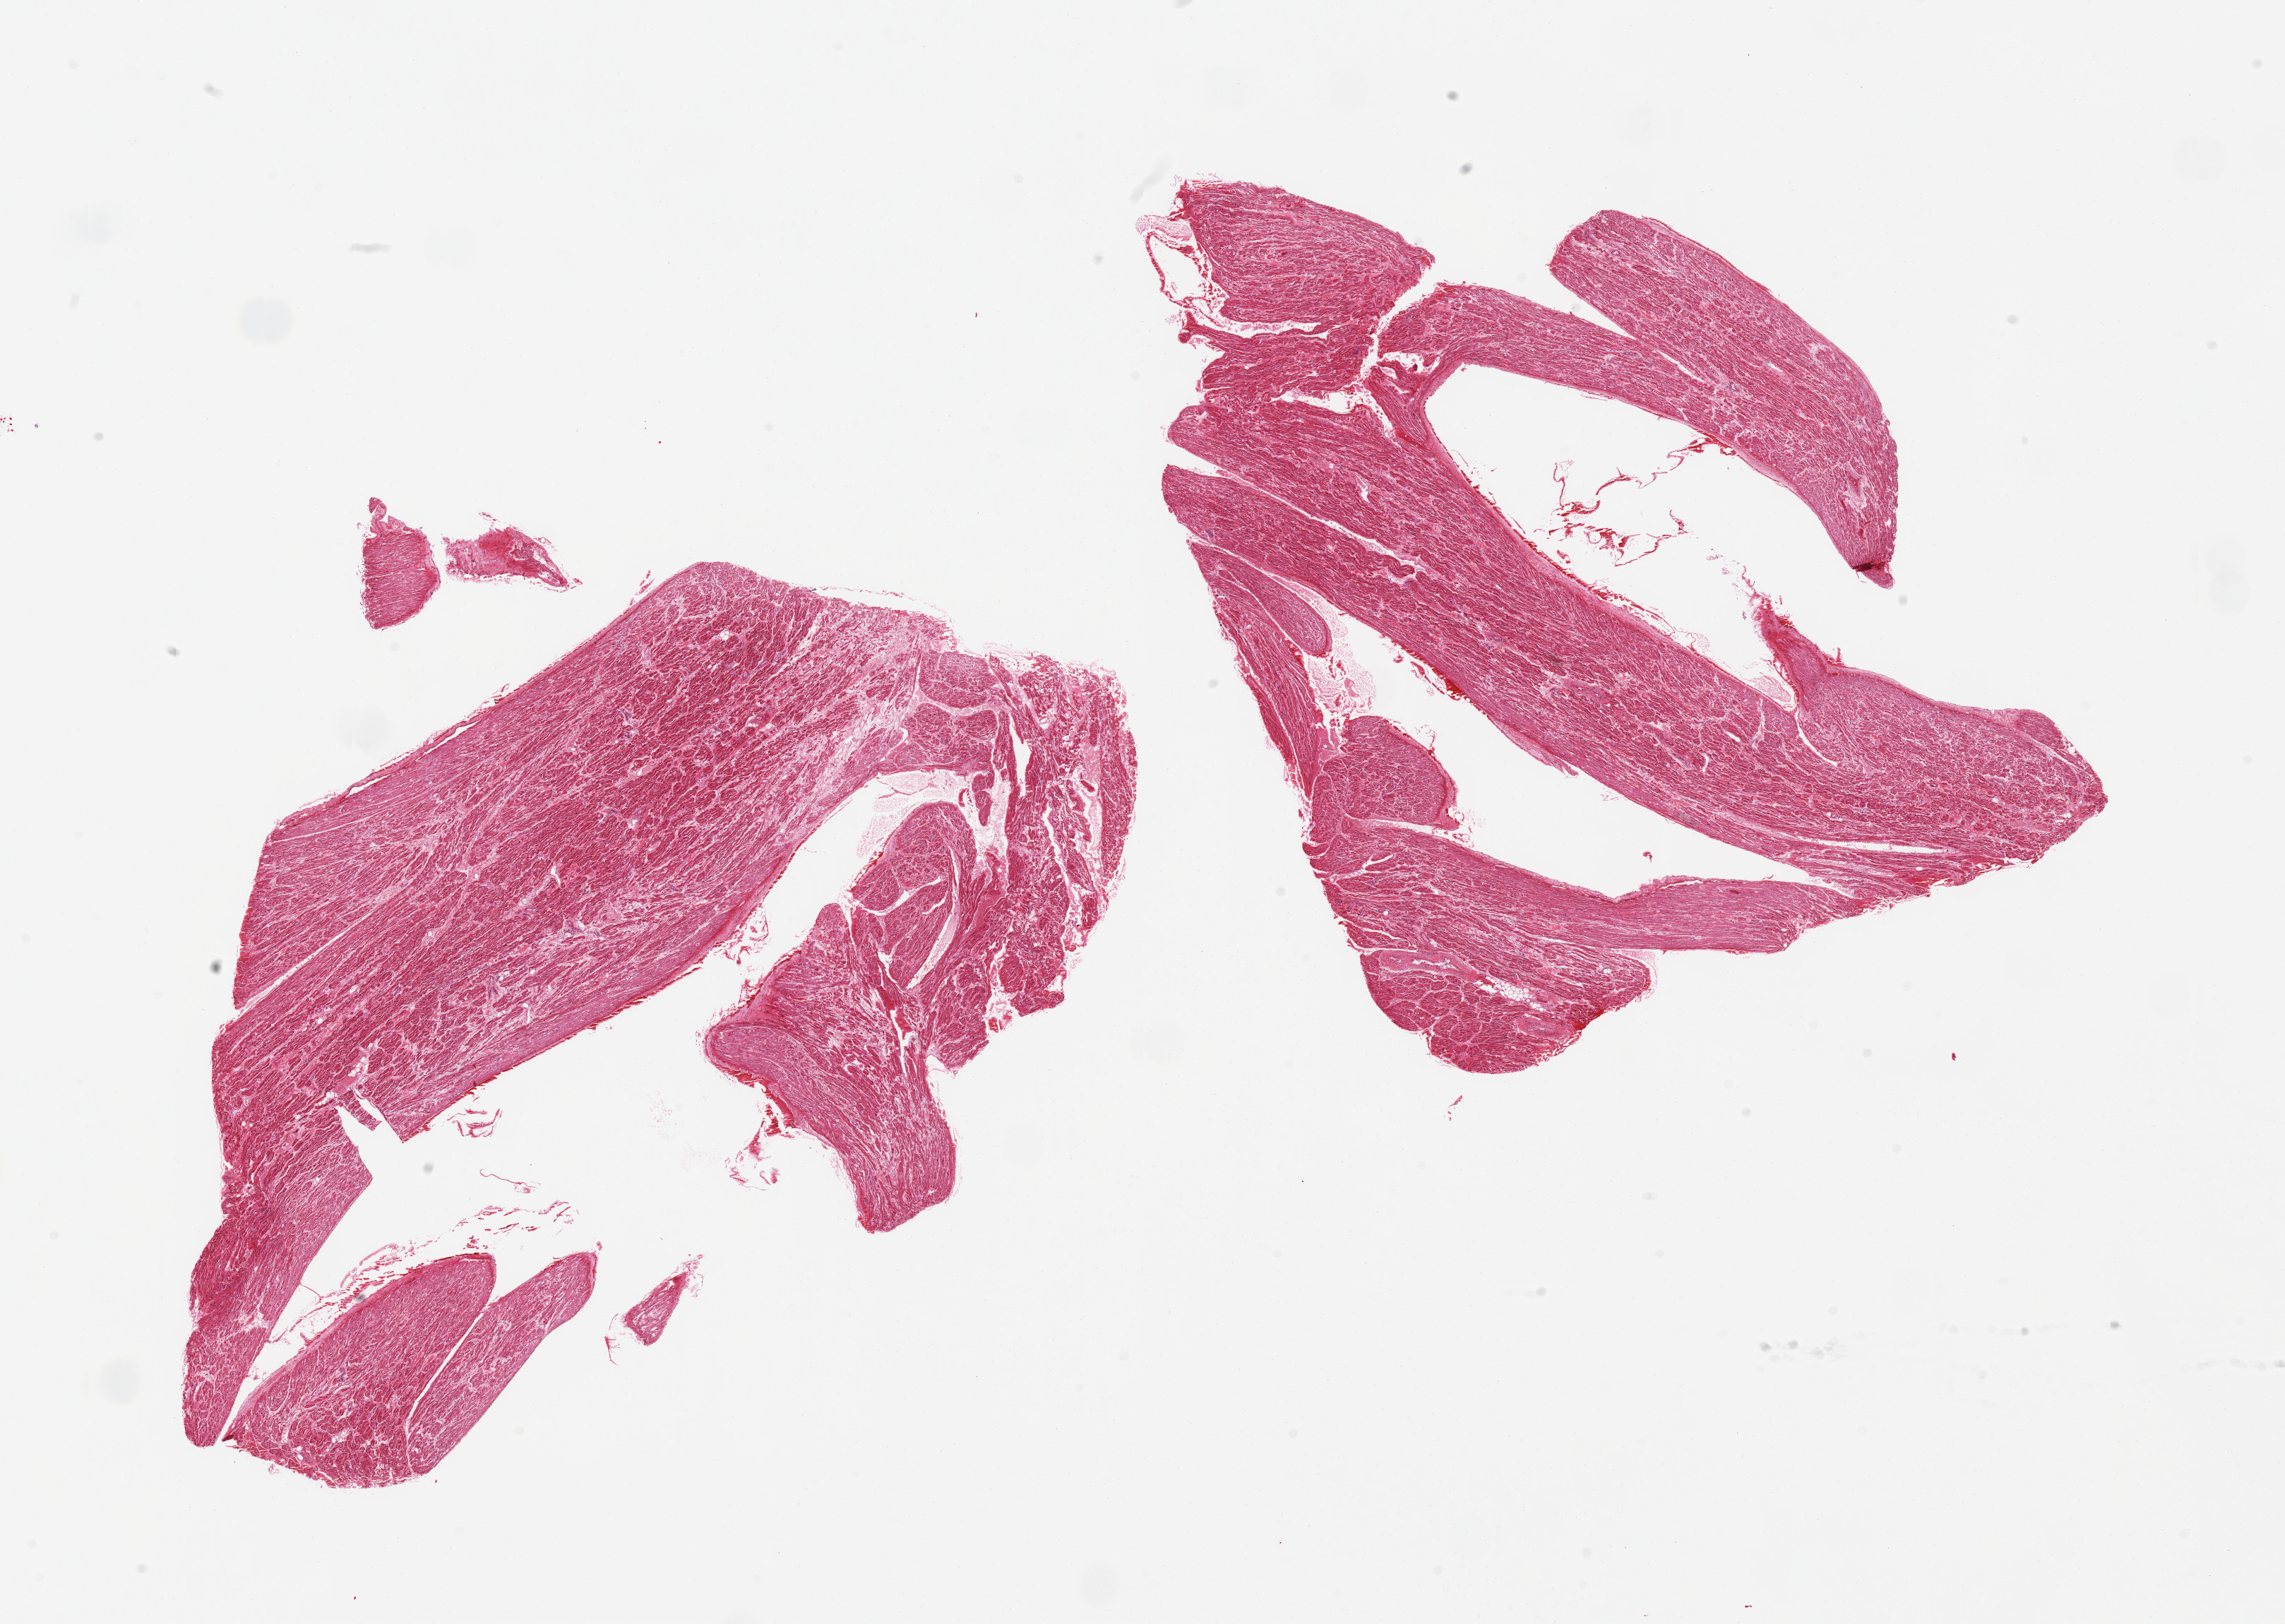
Haematoxylin and eosin whole-slide image, brightfield — whole scanned area (about 25.6 x 18.2 mm) shown as a low-resolution overview. PAXgene-fixed paraffin-embedded (PFPE) section. Sampled site (target tissue): auricular appendage. Donor tissue sample. Donor: female.
- reviewer comment on this tissue sample: 2 pieces, no abnormalities noted